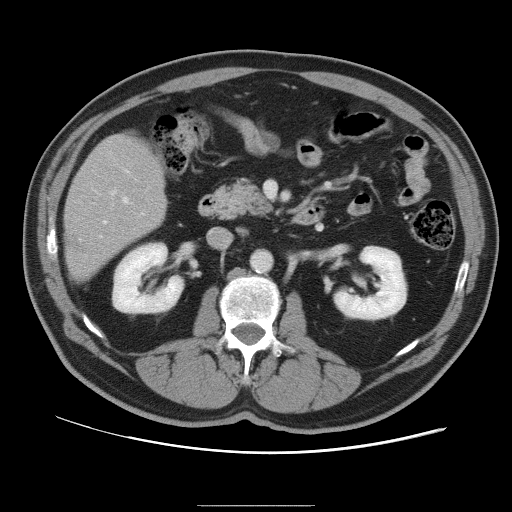
Contrast-enhanced abdominal CT, one axial slice; slice 41 of 105 in the series (ordered by position); intravenous contrast given; soft-tissue window (W 400 / L 40 HU); 5 mm slice thickness; 512 × 512 image matrix, field of view 399 × 399 mm. Male patient, age 64 years. From the clinical record (not read from this slice): diagnosis: colorectal cancer liver metastases, imaged before liver resection; multiple liver metastases: yes; largest metastasis: 3 cm; disease in both lobes: yes.
Annotated regions visible in this slice (expert manual segmentation):
- hepatic veins: bounding box (x1, y1, x2, y2) in pixels: (103, 197, 128, 224)
- liver: (66, 133, 167, 280)
- planned liver remnant (the part of the liver to remain after resection): (67, 133, 166, 260)
- portal vein (with intrahepatic branches): (100, 169, 129, 237)
- liver metastasis: (69, 231, 80, 251)